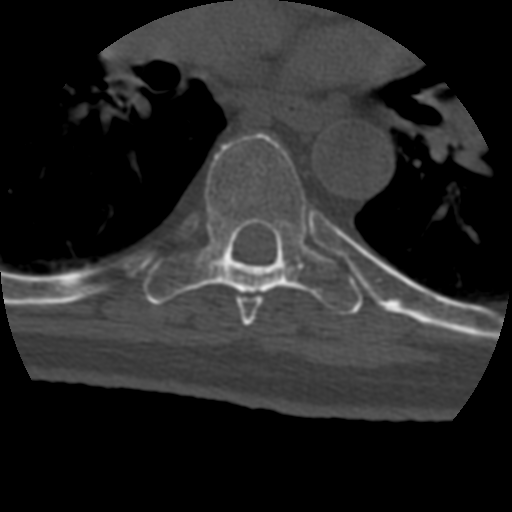
CT including the spine, one axial slice; slice 286 of 399 in the series (ordered by position); reconstruction kernel STANDARD; 120 kVp; bone window (W 1800 / L 400 HU); 1.25 mm slice thickness; 512 × 512 image matrix, field of view 160 × 160 mm. Patient age 69 years. From the clinical record (not read from this slice): primary cancer: prostate.
Outlined on this slice (semi-automatically segmented with operator editing):
- T6 vertebra: box from (x=236, y=296) to (x=262, y=326) px
- T7 vertebra: (x=145, y=133)–(x=363, y=315)